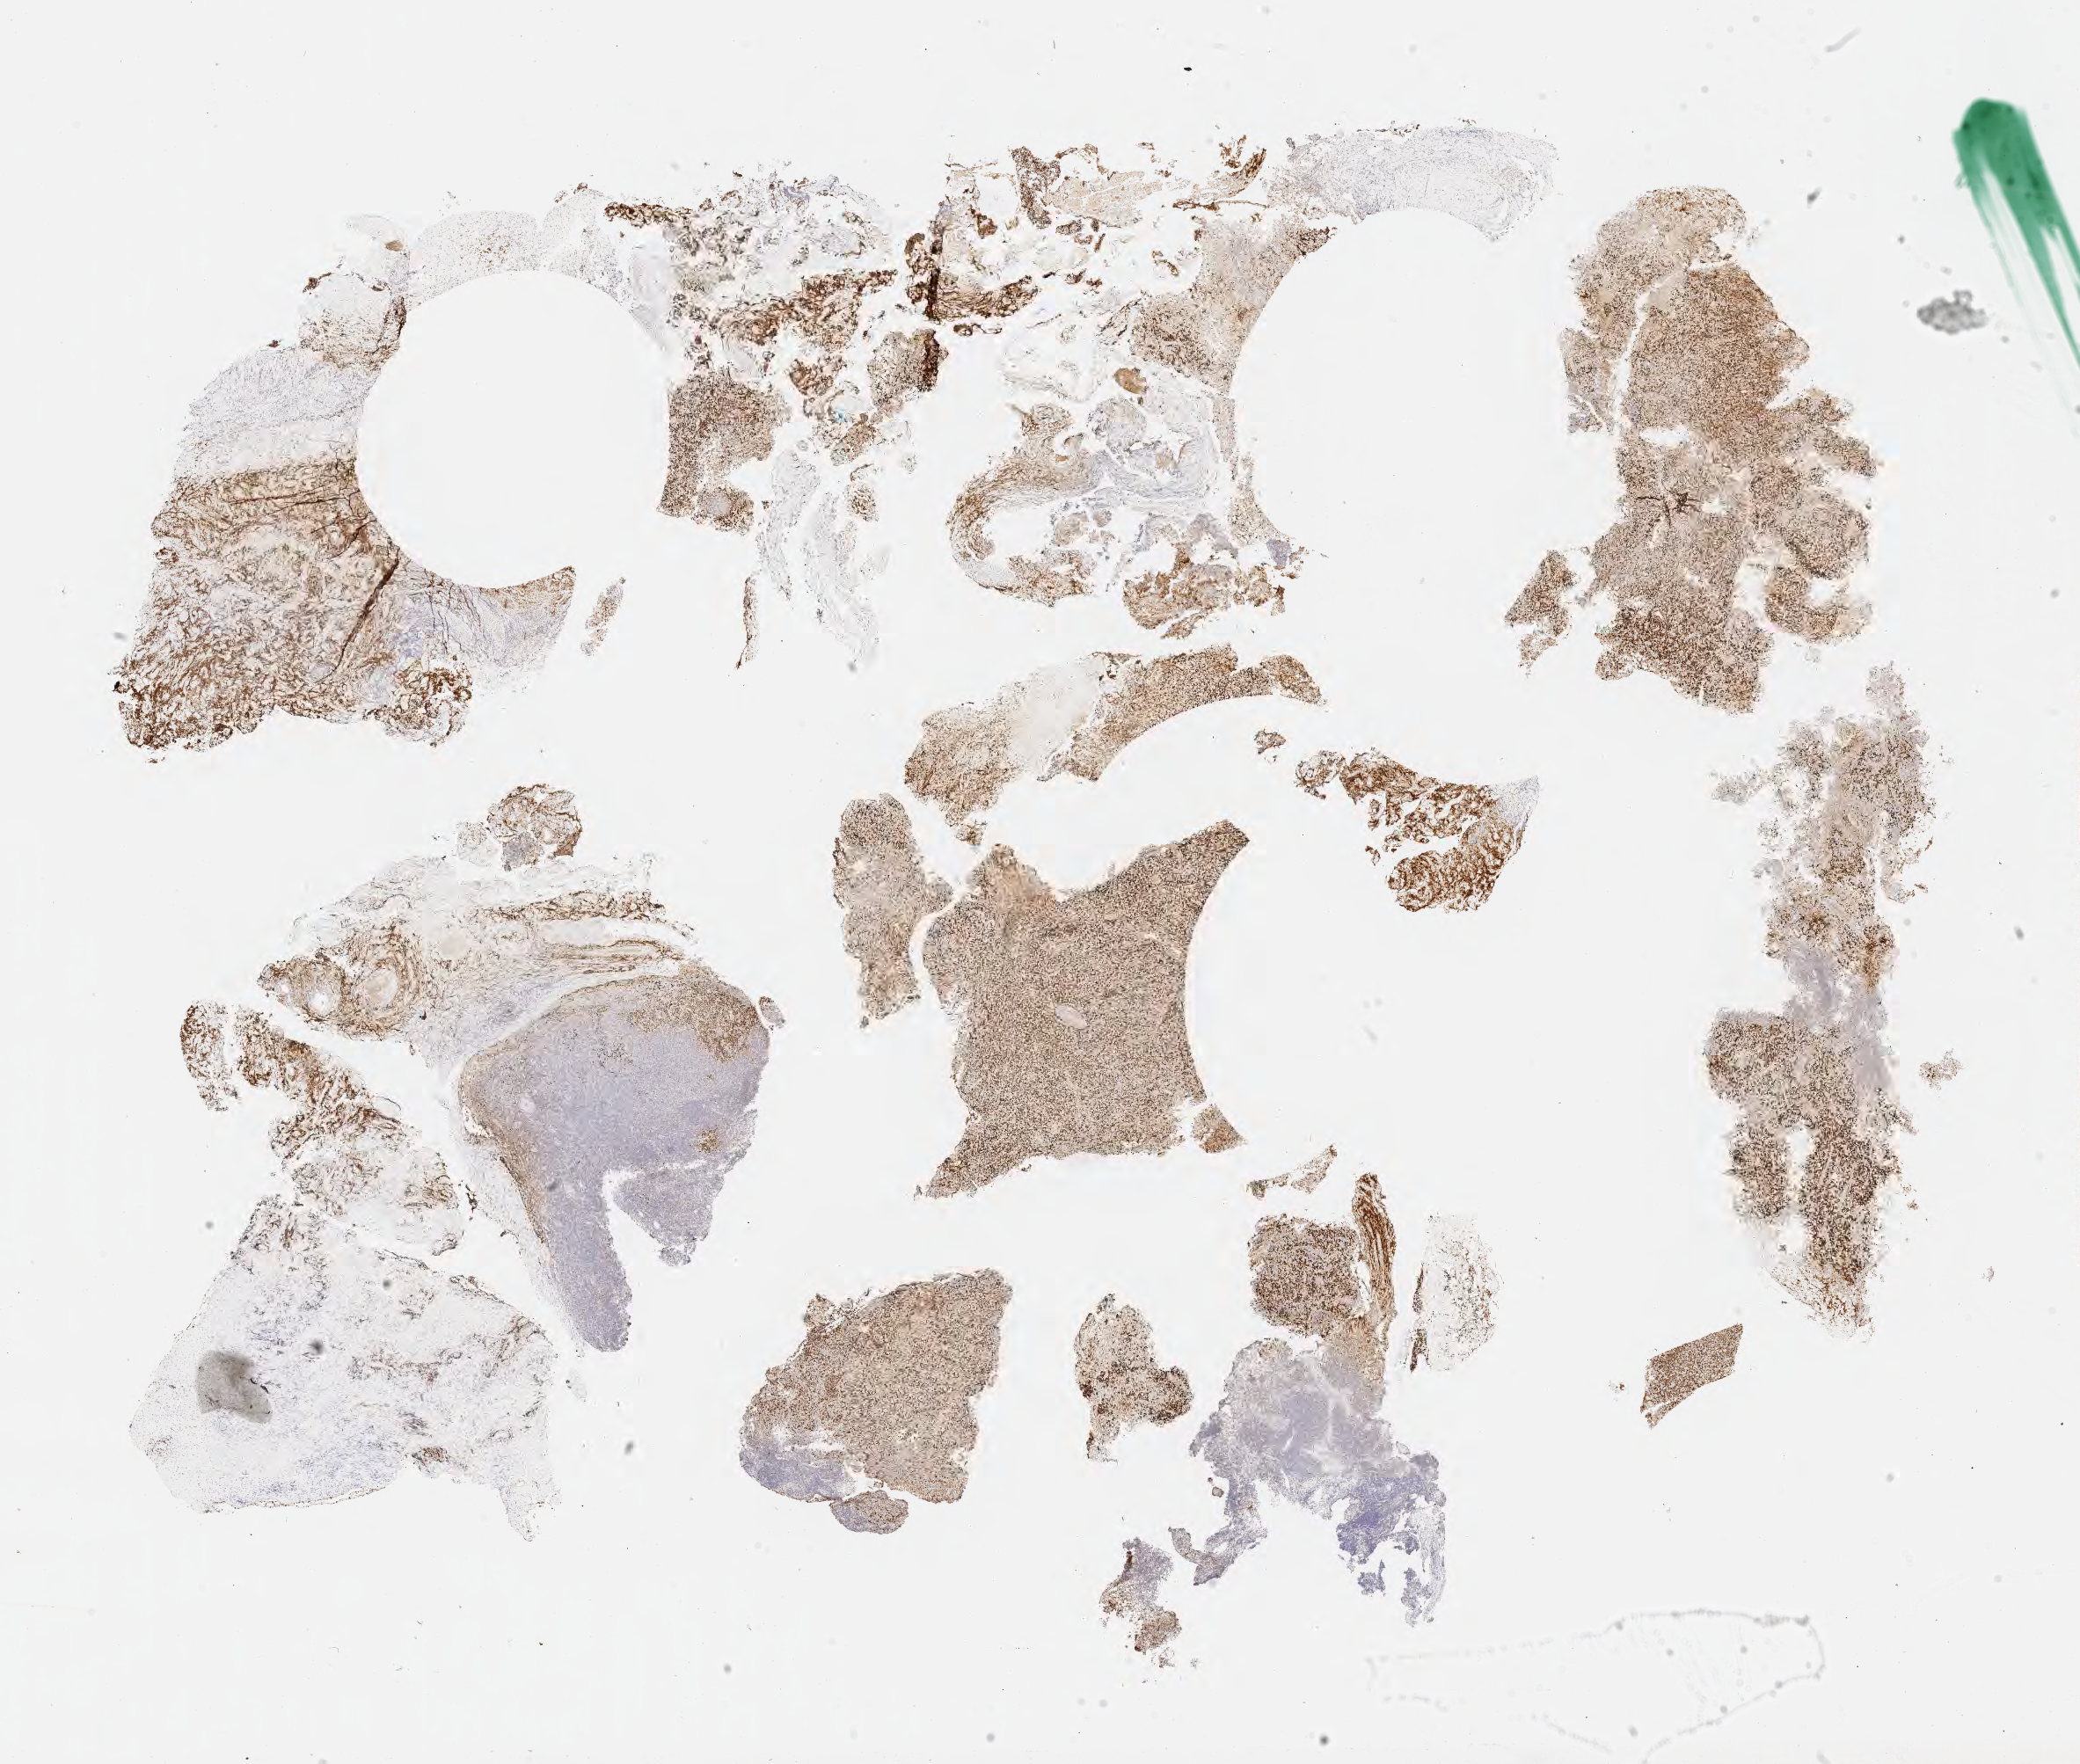
Whole-slide image, immunohistochemical stain for BCL6 — low-resolution overview of the scanned area, about 19.1 x 16.2 mm; tumor tissue; anatomic site: lymph node. Male patient, age 29 years.
Histologic diagnosis: Diffuse large B-cell lymphoma, NOS.